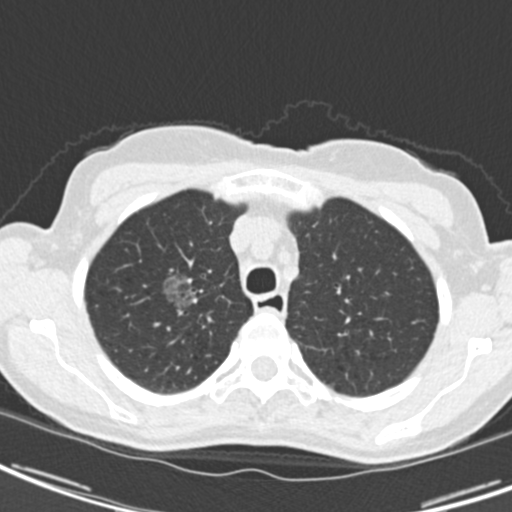
Low-dose screening chest CT, one axial slice; position 158 of 189 along the scan axis; reconstruction kernel B30f; 120 kVp; lung window (W 1500 / L -600 HU); 2 mm slice thickness; 512 × 512 image matrix, field of view 279 × 279 mm.
Structures marked on this image (outlined manually by an expert reader):
- lesion 1 (tumor, upper lobe of right lung): bounding box <161,274,193,310> (left, top, right, bottom; pixels)